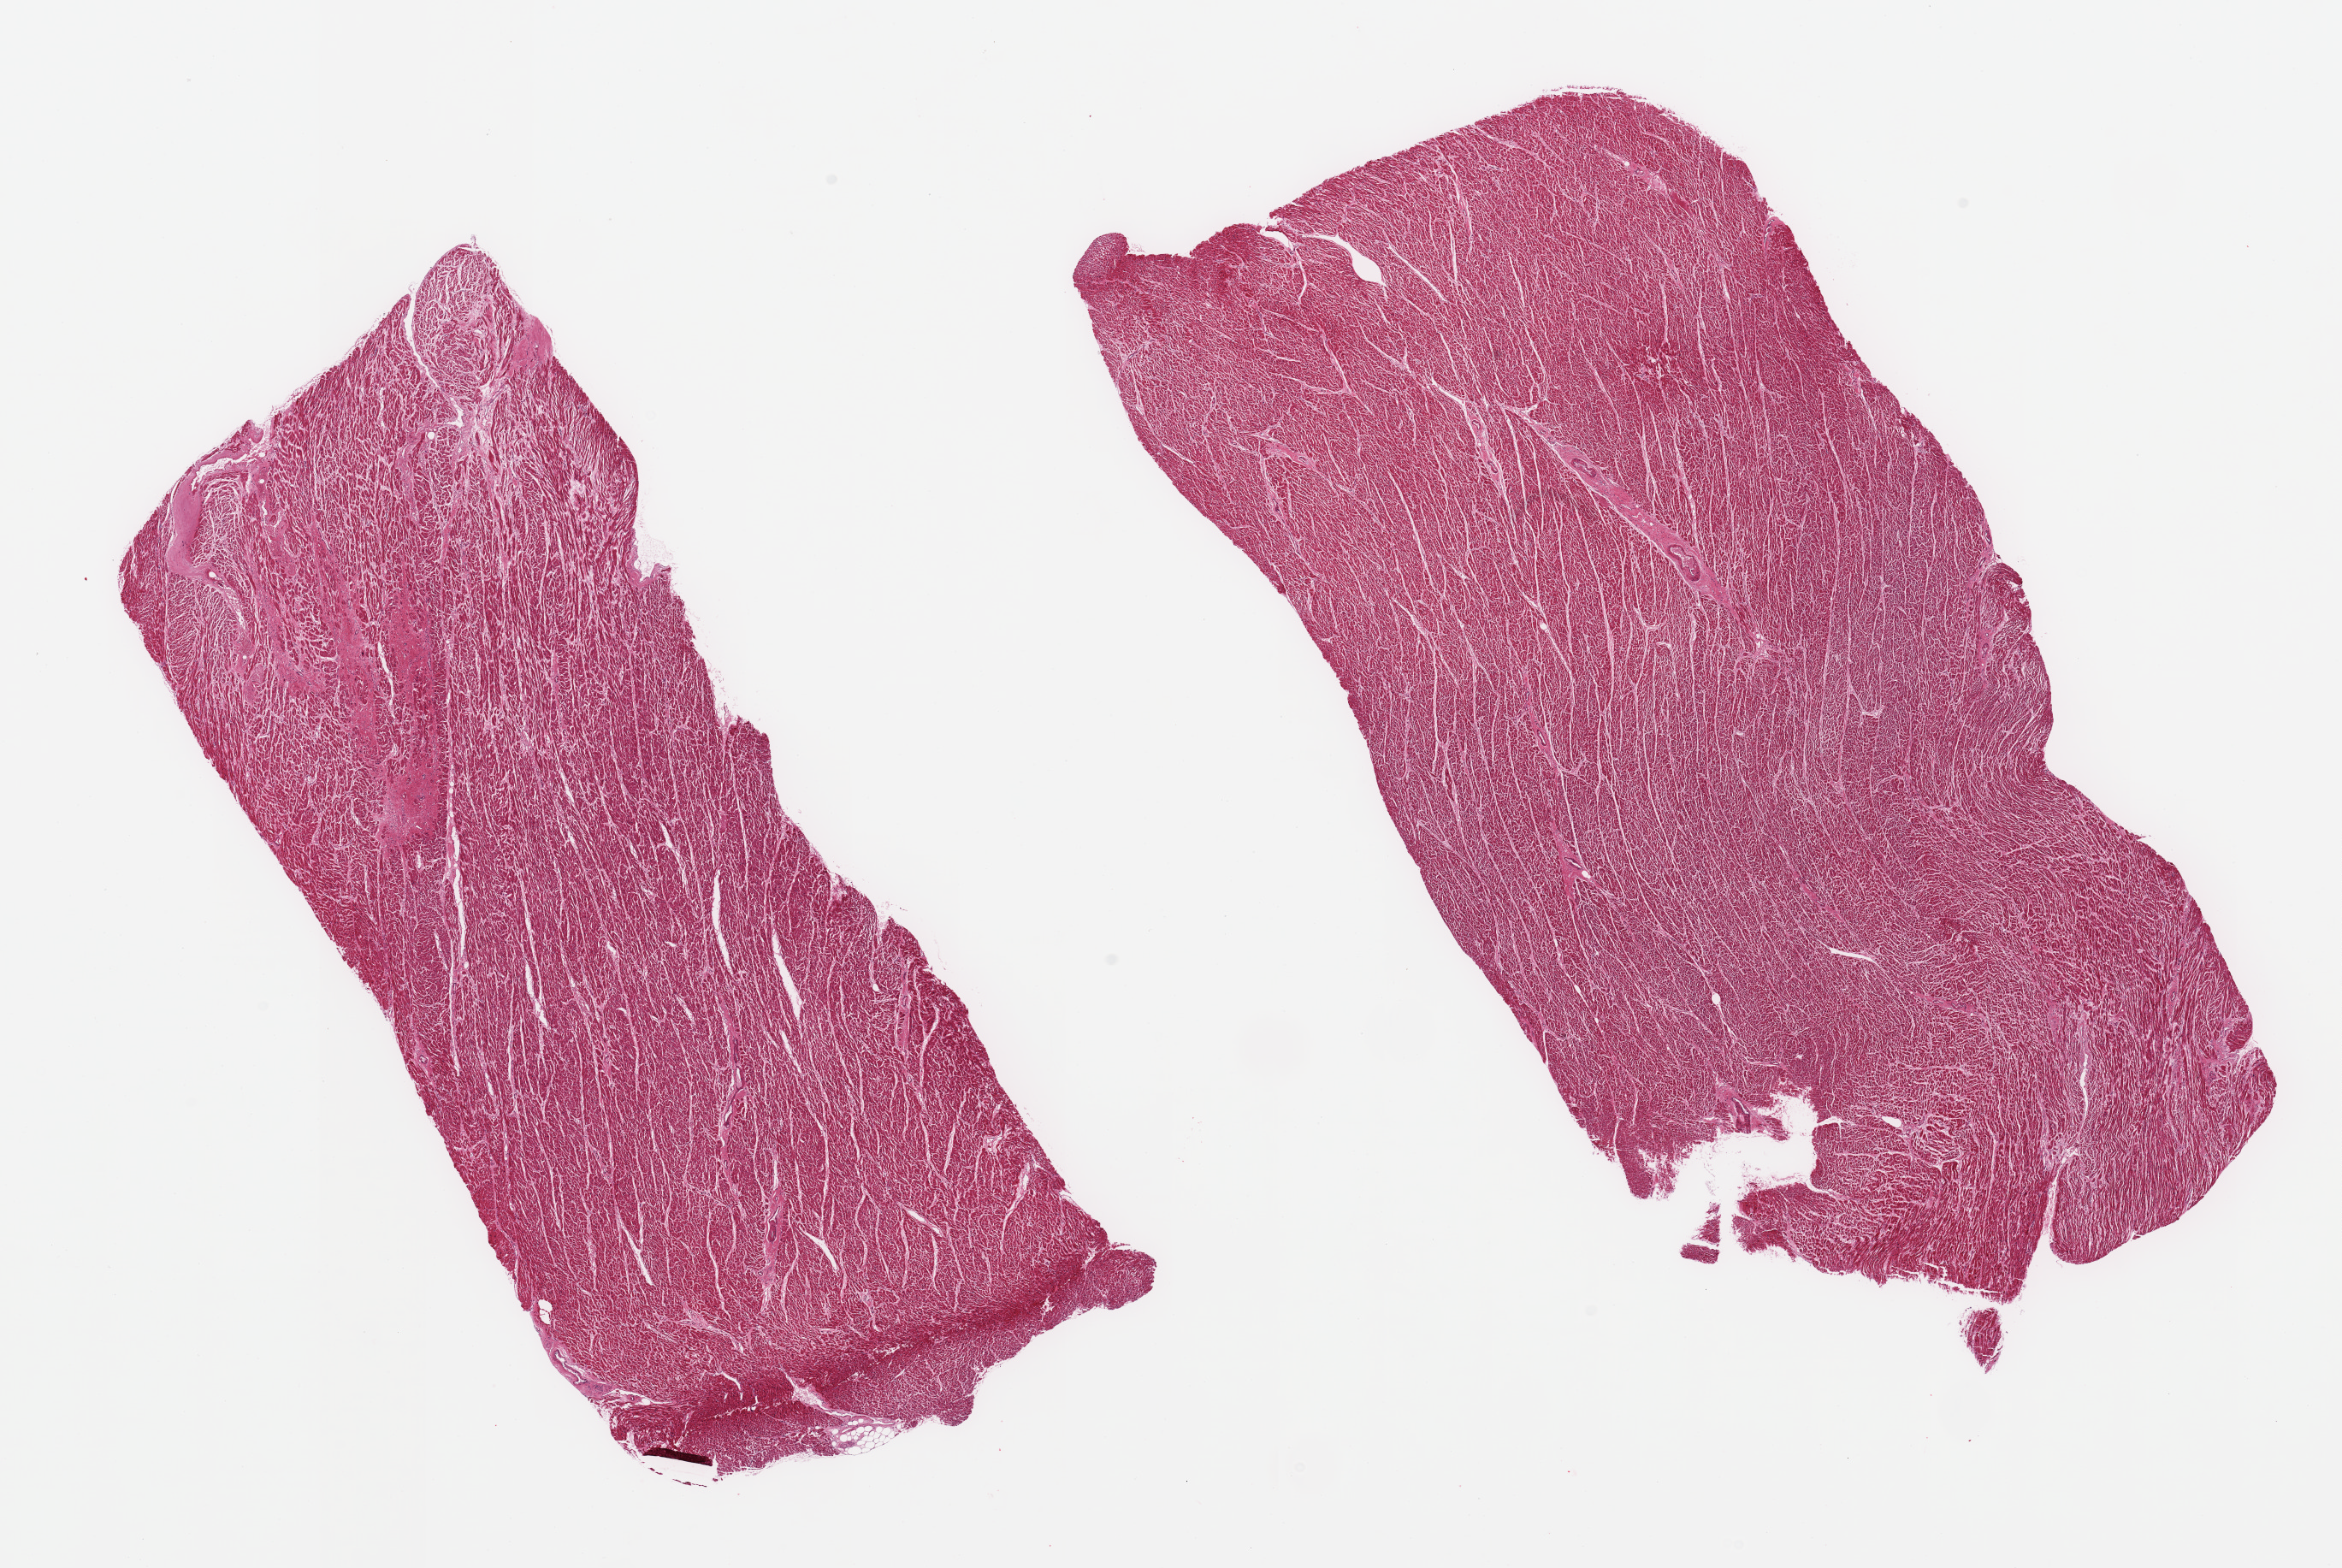
Whole-slide image, haematoxylin and eosin stain, whole scanned area (about 21.7 x 14.5 mm) shown as a low-resolution overview; PAXgene-fixed paraffin-embedded (PFPE) section; sampled site (target tissue): heart; donor tissue sample. Donor: male.
* reviewer comment on this tissue sample: 2 pieces, marked chronic ischemic change, 3mm remote infarct; patchy hyperemic foci suggest acute ischemic events